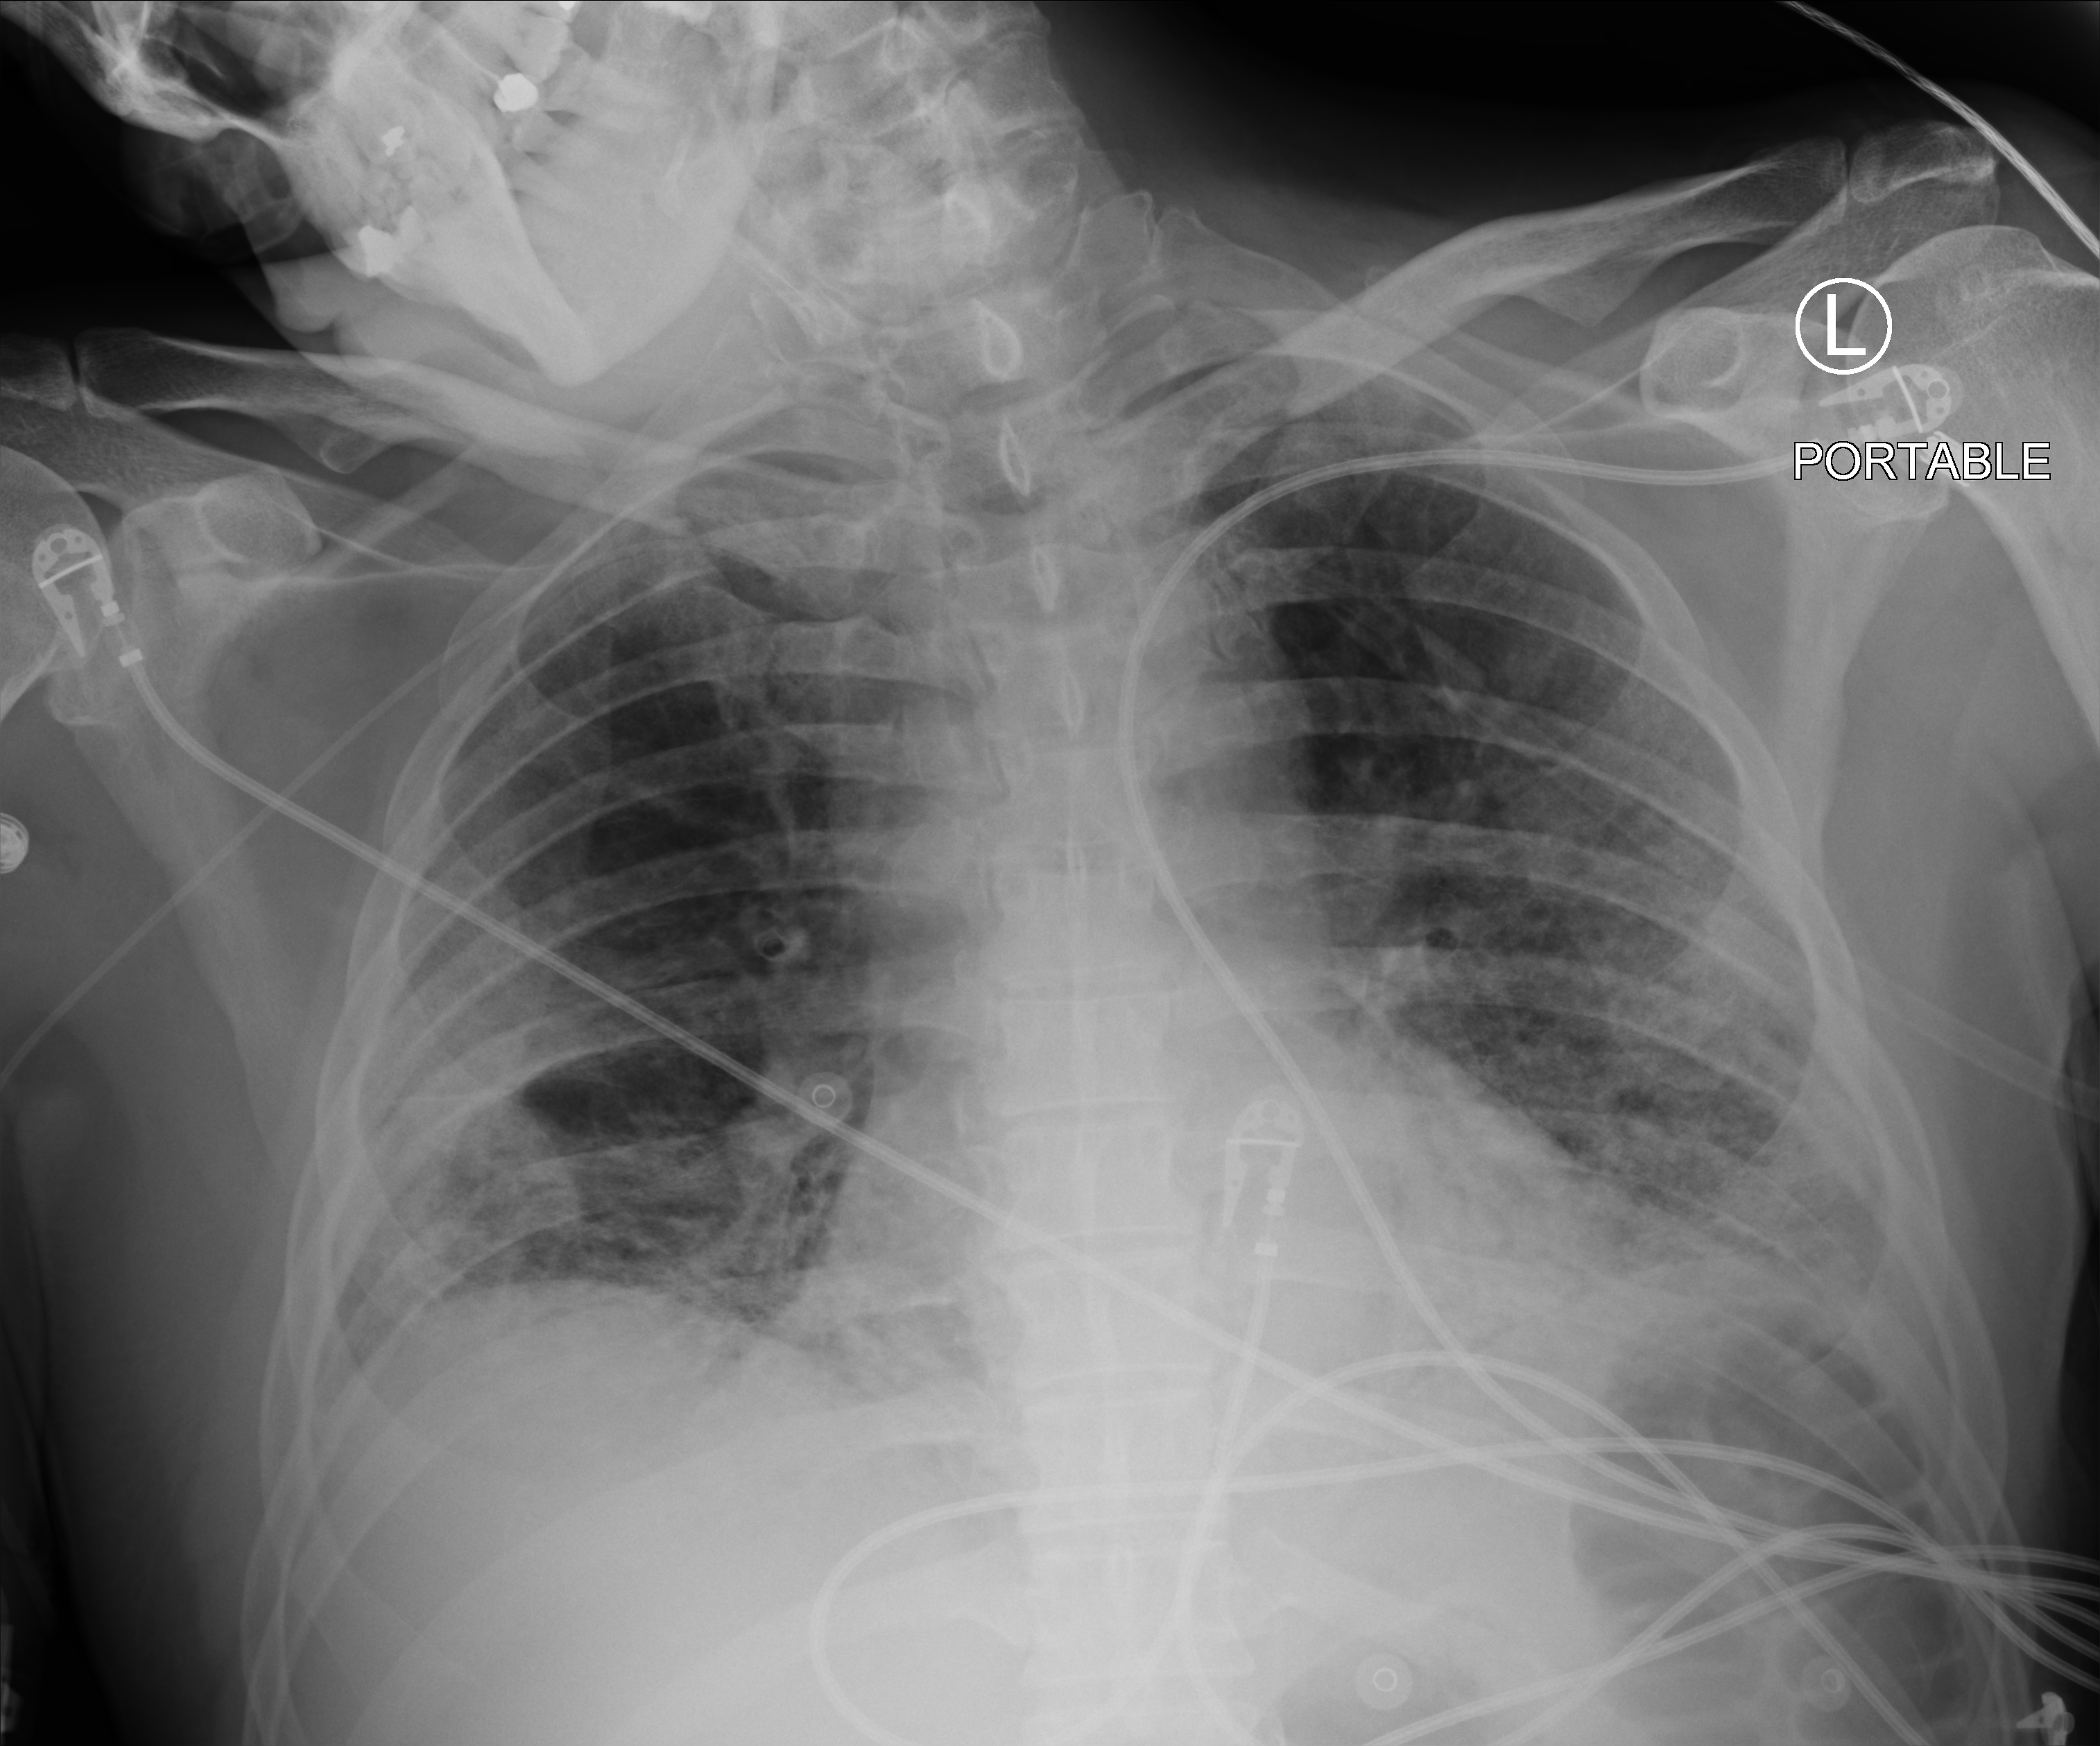
Chest X-ray (portable); anteroposterior (AP) projection. Male patient hospitalised with COVID-19, age 60–74 years.
From the hospital-stay record, not from the radiograph (when in the stay this image was taken is not recorded):
- chronic kidney disease (admission record): no
- admitted to intensive care during this hospital stay: yes
- mechanically ventilated during this hospital stay: yes